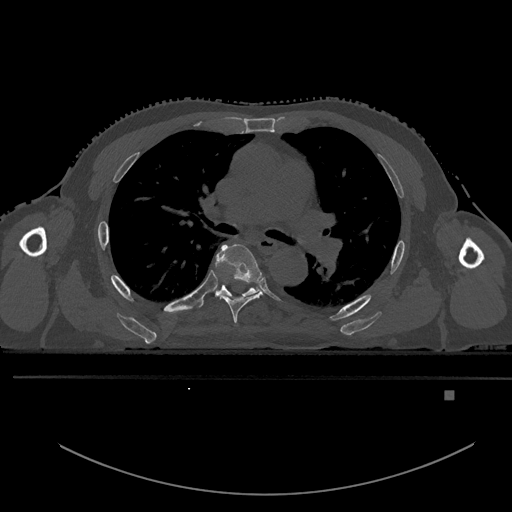
CT including the spine, one axial slice. Position 339 of 969 along the scan axis. Bone window (W 1800 / L 400 HU). 0.5 mm slice thickness. 512 × 512 image matrix. Patient: male, 82 years. Case-level facts recorded for this patient, not image findings: primary cancer: prostate; vertebrae with lytic lesions (as recorded): T11, T9, T8, T2.
Structures marked on this image (semi-automatically segmented with operator editing):
- T5 vertebra: bounding box <214,244,263,324> (left, top, right, bottom; pixels)
- T6 vertebra: <198,279,260,307>